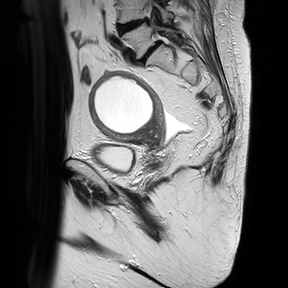
Pelvic MRI for cervical cancer, one sagittal slice. Slice 12 of 30 in the series (ordered by position). T2-weighted. 1.5 T. TE 100 ms, TR 4816.3 ms. 288 × 288 image matrix, field of view 300 × 300 mm. Female patient, age 74 years.
Outlined on this slice (outlined manually by an expert reader):
- uterus and cervix: box from (x=87, y=69) to (x=167, y=147) px